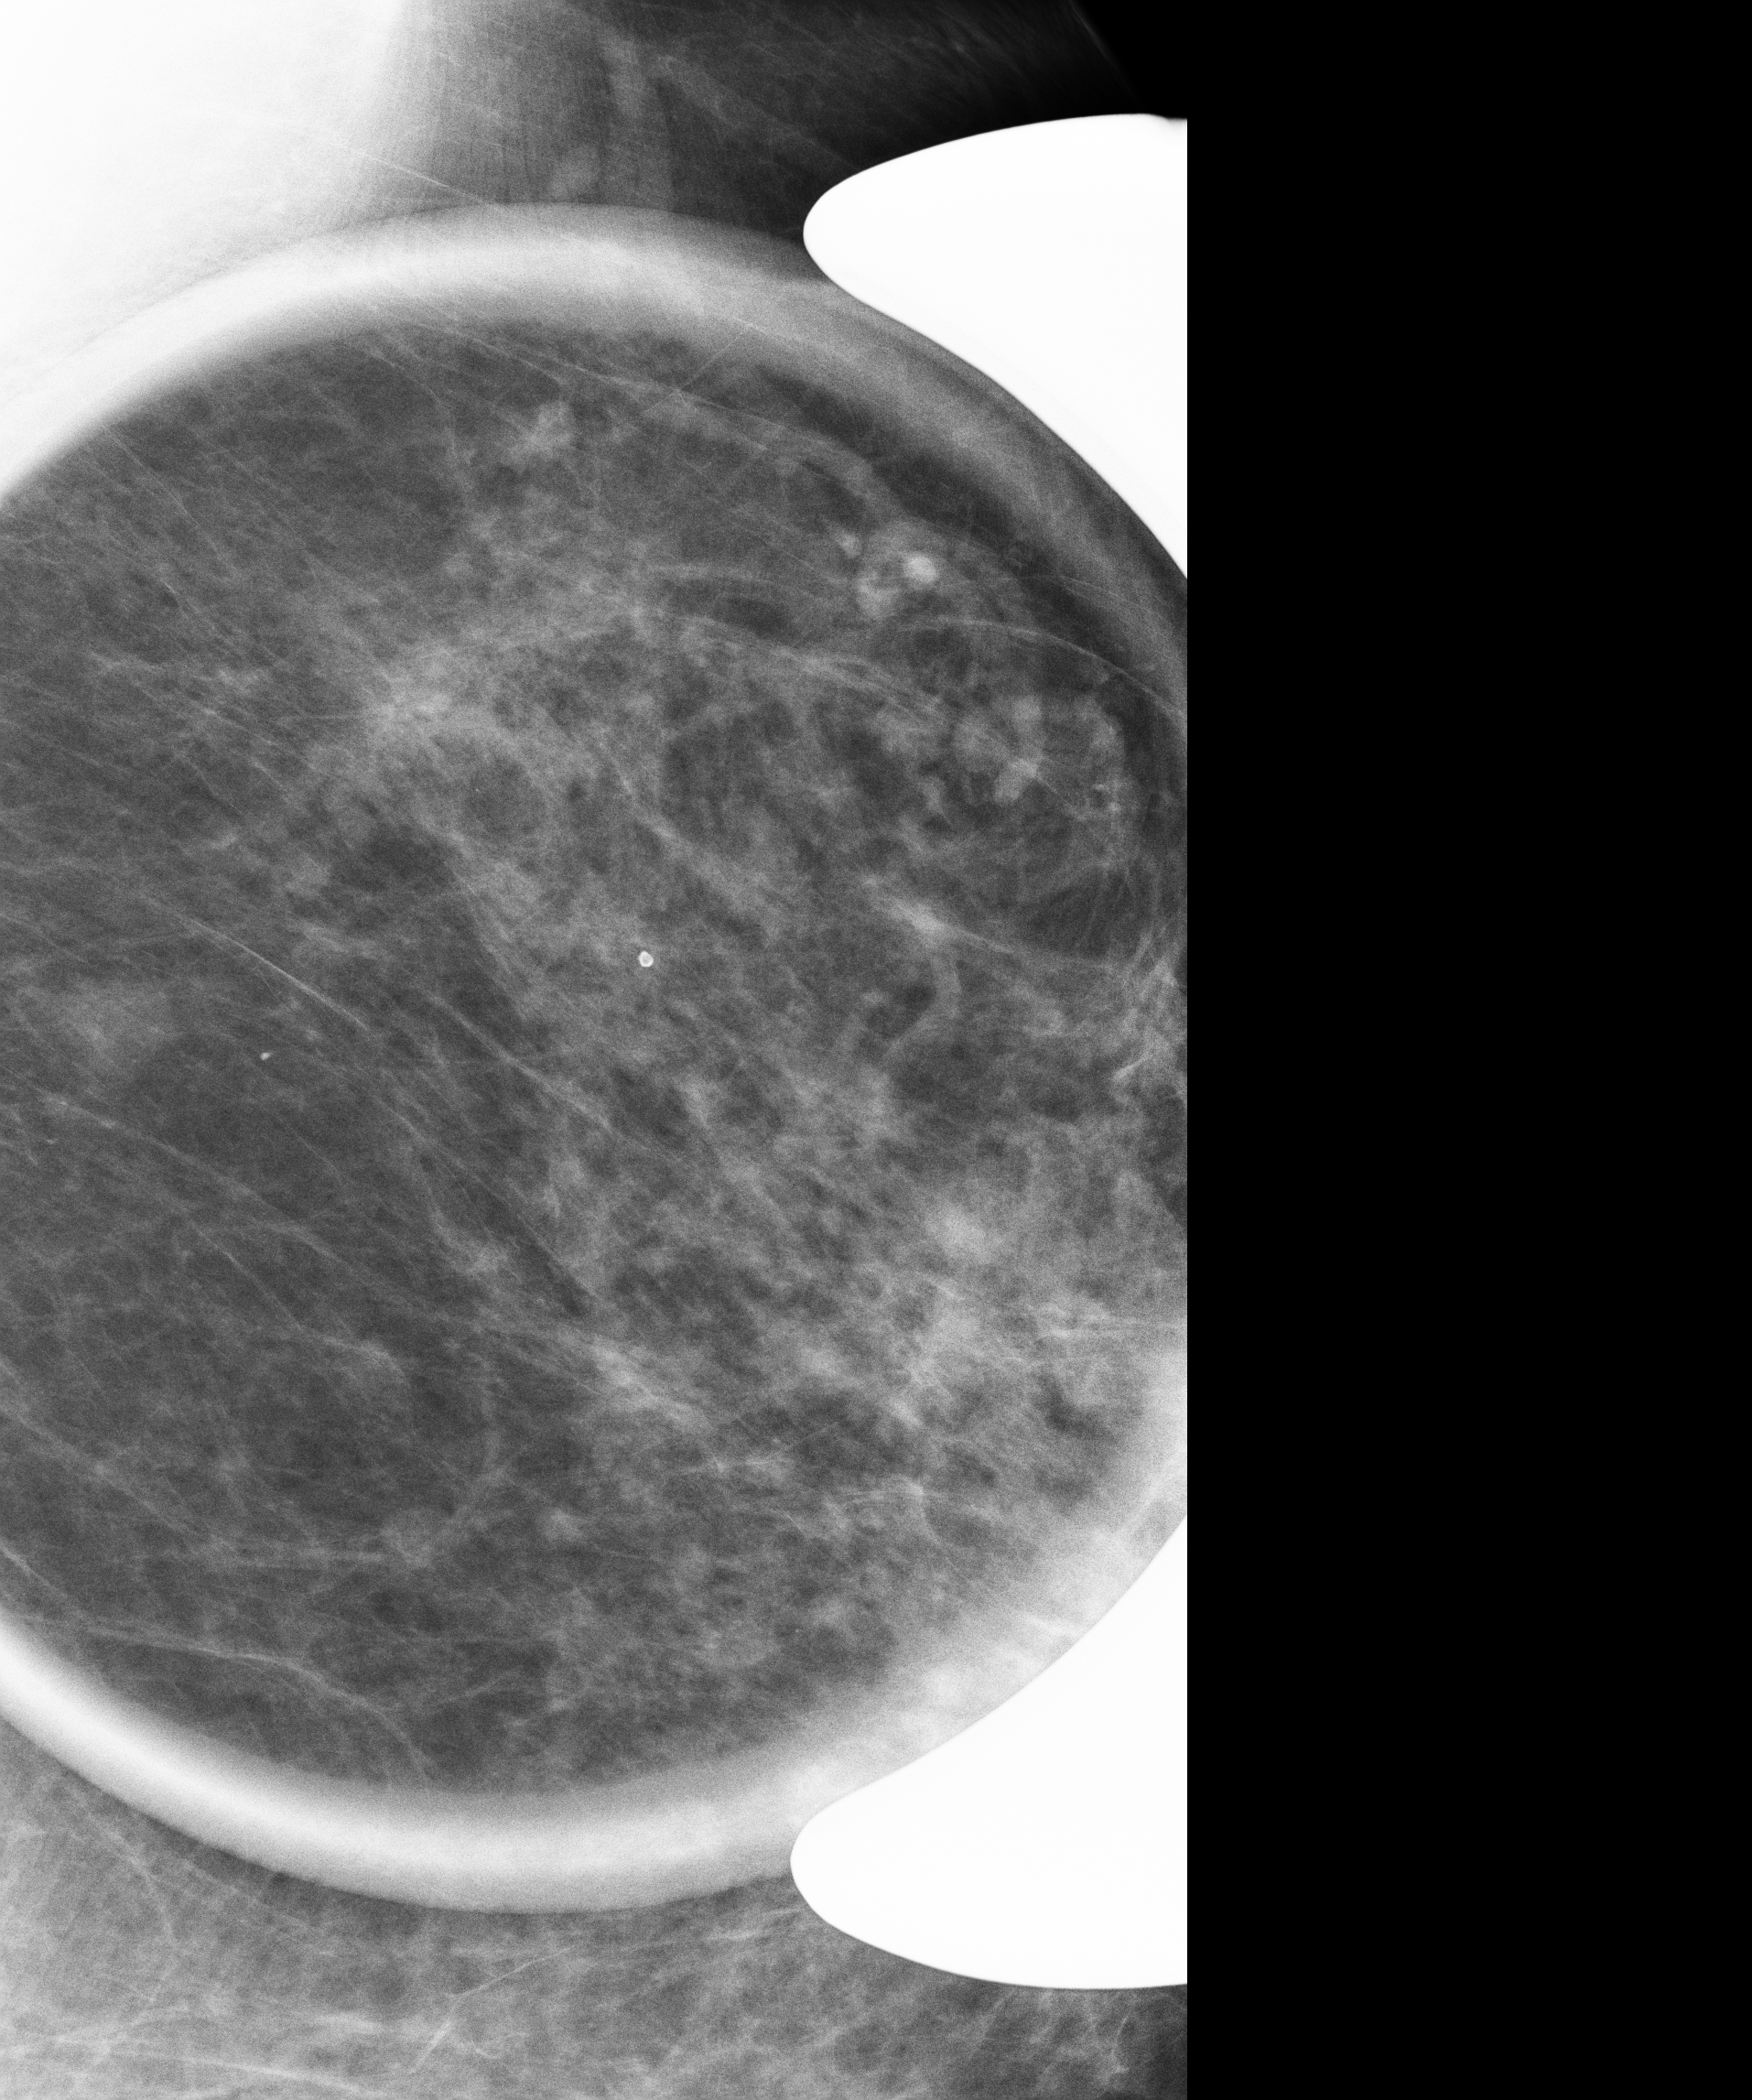
Full-field digital mammogram (FFDM), left breast, cranio-caudal projection, diagnostic work-up study, system: Senographe Essential ADS_56.21.3. Patient: female, 53 years.
Breast density at the screening exam (both breasts): heterogeneously dense (BI-RADS density category c). Final BI-RADS assessment for this screening round (tomosynthesis exam, both breasts): category 4. Recall: recalled for additional imaging after this screen.